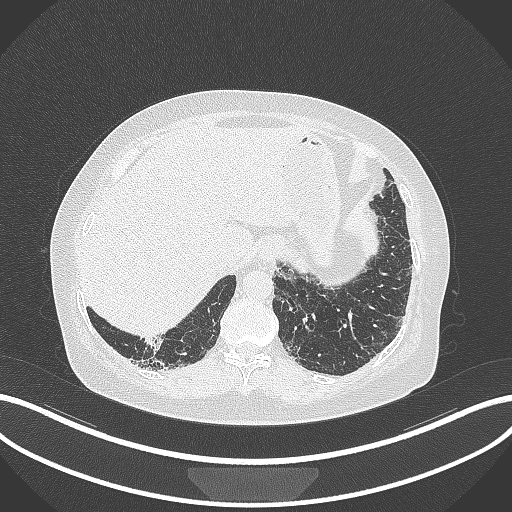
Chest CT, one axial slice; position 9 of 296 along the scan axis; reconstruction kernel B70f; lung window (W 1500 / L -600 HU); 1 mm slice thickness; 512 × 512 image matrix, field of view 400 × 400 mm. Patient: female, 65 years. Case-level facts recorded for this patient, not image findings: clinical TNM (as recorded): T2b N1 M0; histopathological grade: G1.
Outlined on this slice (rectangle marked by the reading radiologist):
- lung tumour (recorded histology: adenocarcinoma): box from (x=140, y=331) to (x=167, y=357) px